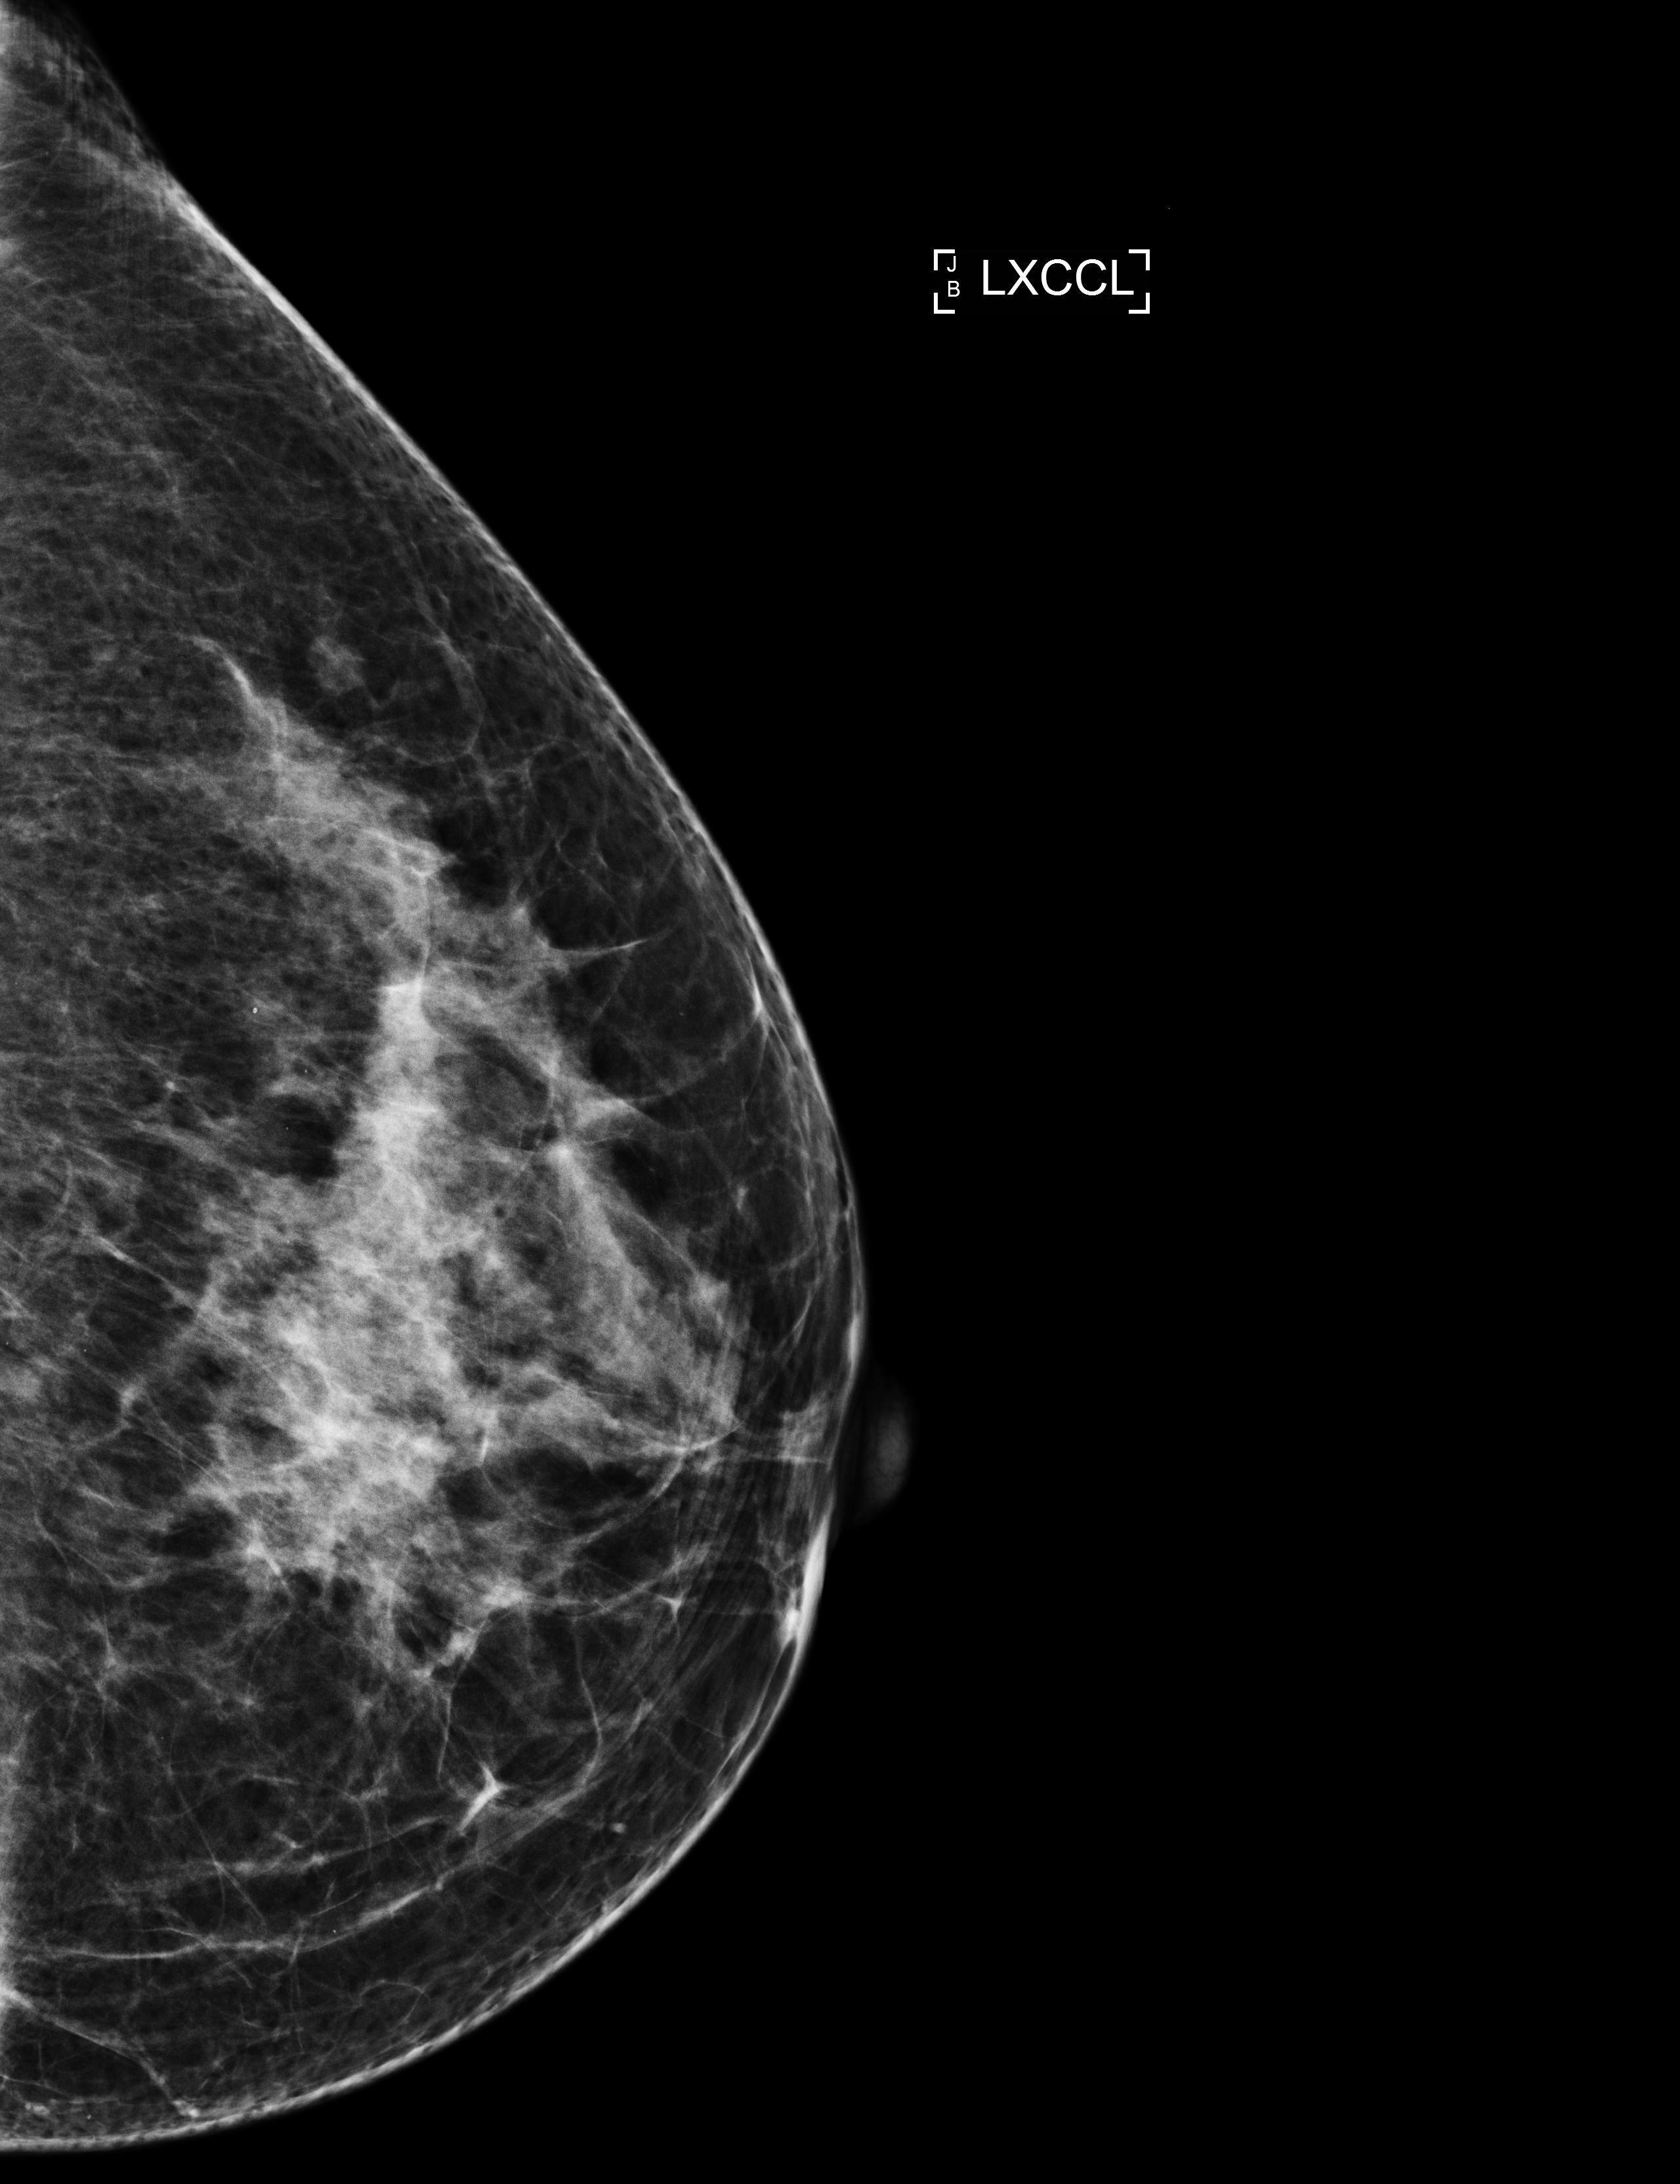
Annual screening mammography examination; system: Selenia Dimensions. Female patient, age 61 years.
Image type: full-field digital mammogram. Breast: left. Projection: exaggerated CC view (lateral).